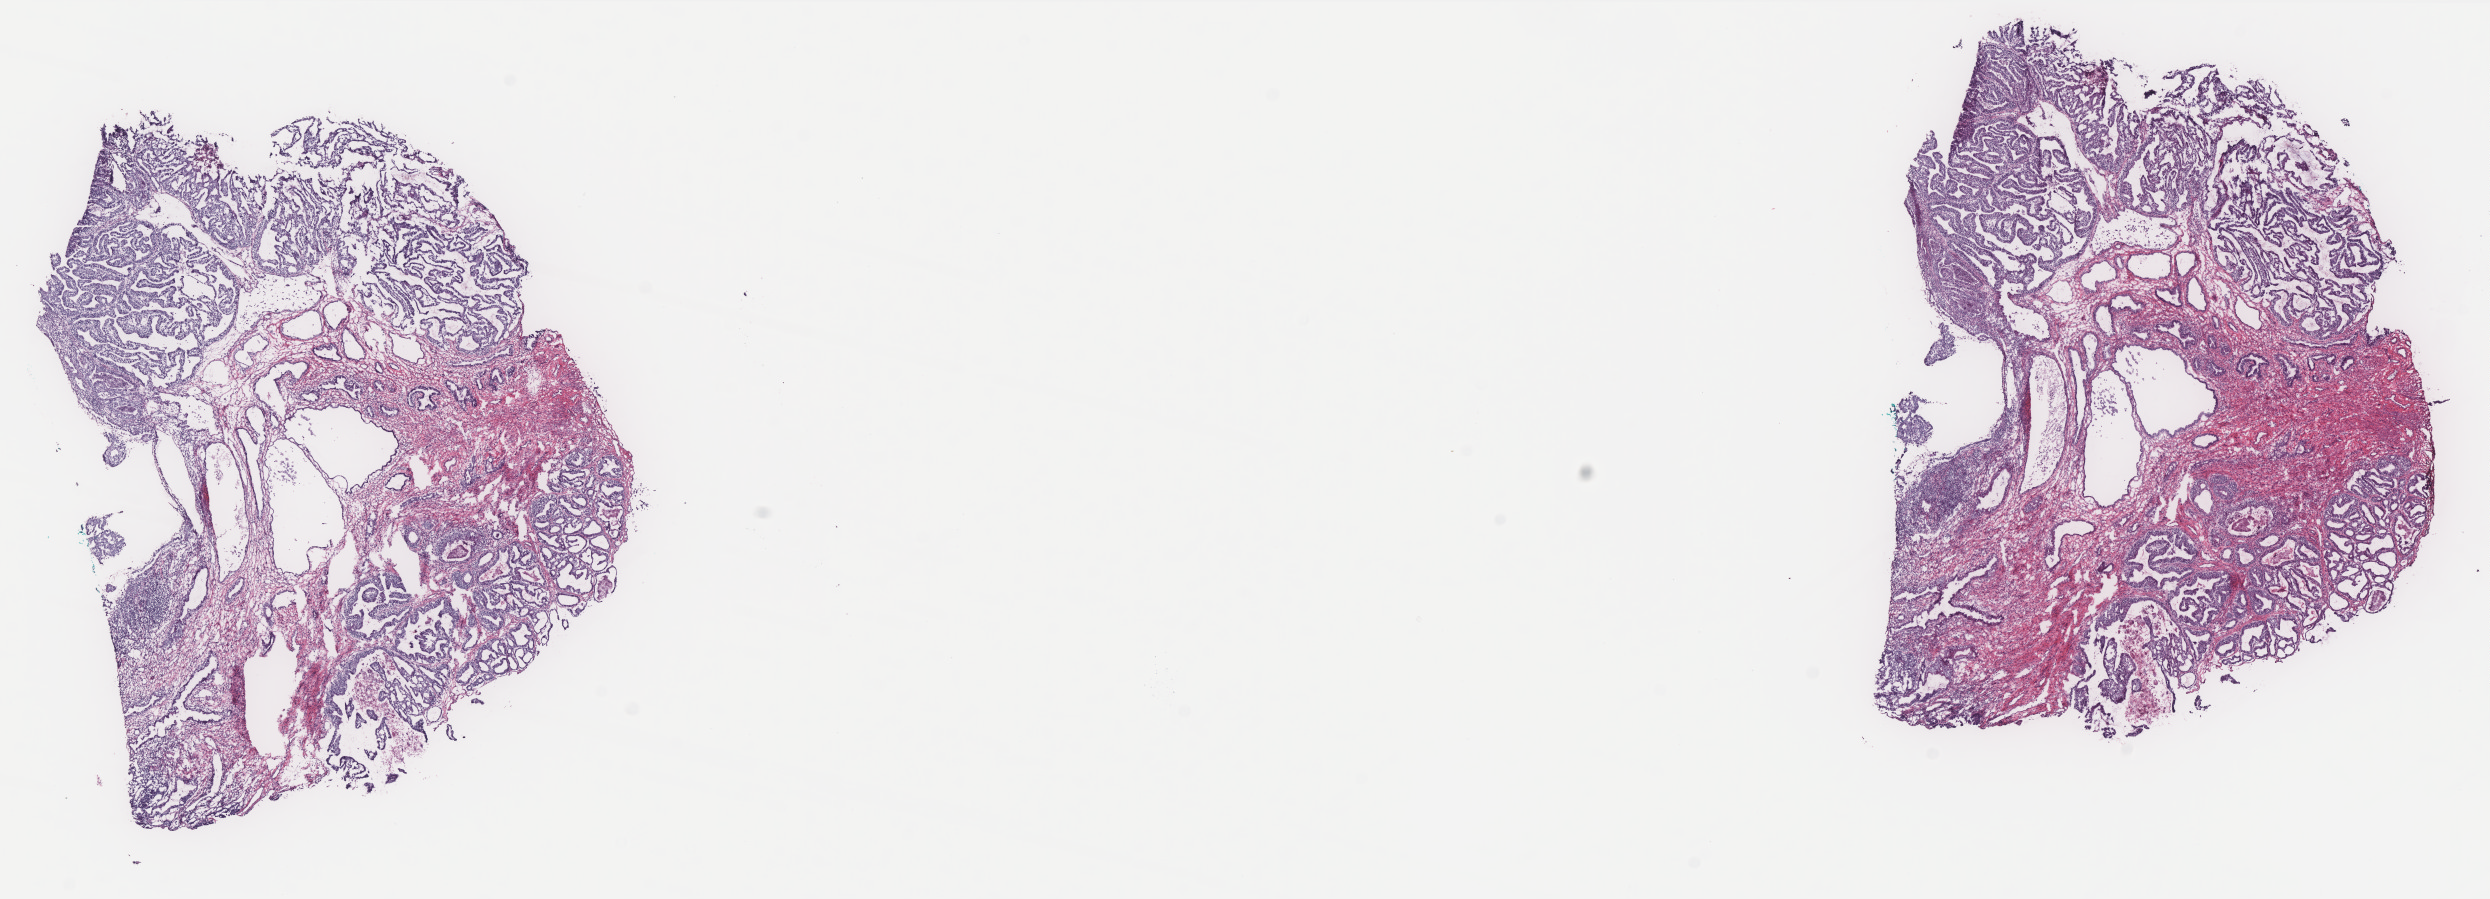
H&E-stained whole-slide image, low-resolution overview of the scanned area, about 20.0 x 7.2 mm (acquisition: 40x scan), frozen section, uterus, primary tumour sample. Patient: female, age at initial diagnosis 68 years. Histologic grade: G1 (well differentiated). Pathologist review of this section (percent, as recorded): tumour cells 50%, tumour nuclei 50%, normal cells 10%, stromal cells 40%, necrosis 0%. Infiltration values recorded for this section: lymphocyte infiltration 0%, monocyte infiltration 0%, neutrophil infiltration 0%.
FIGO stage: IB. Pathologic diagnosis: Endometrioid adenocarcinoma, NOS (endometrium).